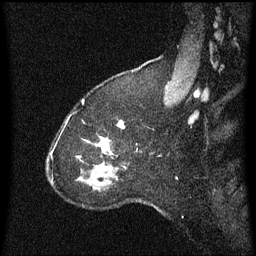
Breast MRI (dynamic contrast-enhanced), one sagittal slice. Slice 48 of 60 in the series (ordered by position). Dynamic contrast-enhanced series, image 2 of 3 at this slice position (ordered by acquisition). 1.5 T. TE 4.2 ms, TR 8.4 ms. 2 mm slice thickness. 256 × 256 image matrix, field of view 200 × 200 mm. Female patient, age 37 years. From the clinical record (not read from this slice): setting: breast cancer imaged before/during neoadjuvant chemotherapy; receptor status: HR-positive, HER2-negative.
Outlined on this slice (semi-automatic segmentation, software-assisted and operator-edited):
- analysis volume of interest (the breast-tissue region the enhancement analysis was run in; not a lesion): box from (x=95, y=122) to (x=124, y=171) px
- tumour enhancement mask (voxels above the 70 % enhancement threshold inside the analysis volume of interest): (x=120, y=122)–(x=123, y=125)